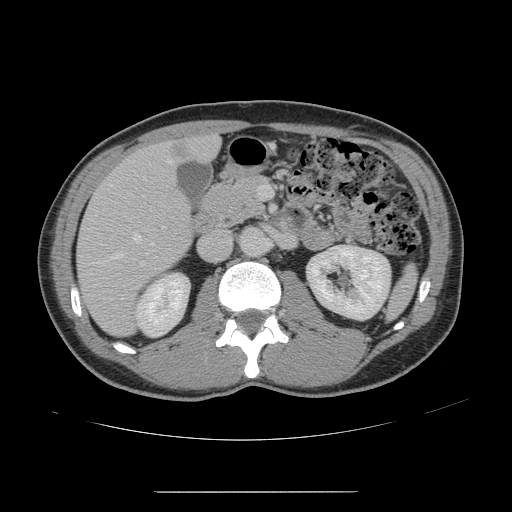
Contrast-enhanced abdominal CT, one axial slice; position 70 of 178 along the scan axis; soft-tissue window (W 400 / L 40 HU); 2.5 mm slice thickness; 512 × 512 image matrix, field of view 401 × 401 mm. Male patient, age 53 years. From the clinical record (not read from this slice): diagnosis: colorectal cancer liver metastases, imaged before liver resection; multiple liver metastases: yes; largest metastasis: 2.4 cm; disease in both lobes: no.
Outlined on this slice (manually delineated by an expert):
- hepatic veins: bounding box [x1, y1, x2, y2] px = [93, 160, 171, 307]
- liver: [78, 137, 219, 335]
- planned liver remnant (the part of the liver to remain after resection): [194, 137, 219, 160]
- portal vein (with intrahepatic branches): [143, 185, 267, 198]
- liver metastasis: [173, 144, 188, 159]